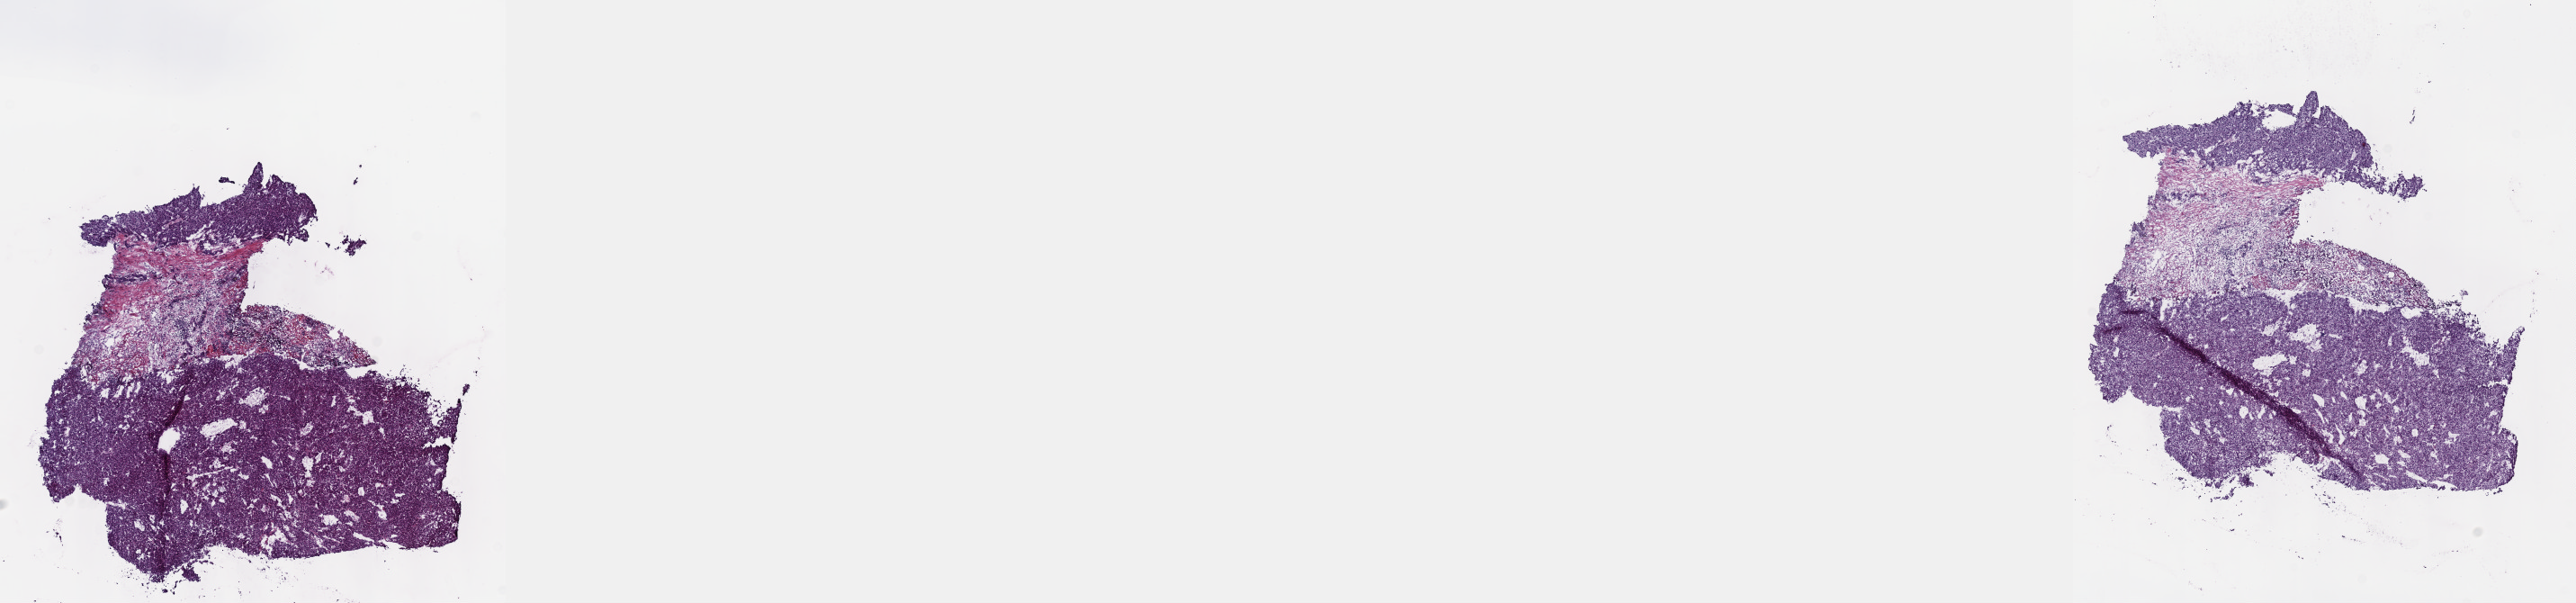
Digitized Hematoxylin and eosin (H&E) stained tissue section (whole slide) — shown as a low-resolution overview of the whole scanned area (about 23.1 x 5.4 mm, slide scanned at 40x). Frozen section. Sample: primary tumour, liver. Female, age 82 years at initial diagnosis. Histologic grade: G2 (moderately differentiated). Composition of this section per pathologist review: tumour cells 80%, tumour nuclei 85%, normal cells 0%, stromal cells 20%, necrosis 0%. Inflammatory infiltration, as recorded: lymphocyte infiltration 0%, monocyte infiltration 0%, neutrophil infiltration 0%.
Diagnosis: Hepatocellular carcinoma, NOS. AJCC pathologic stage: II (6th edition).